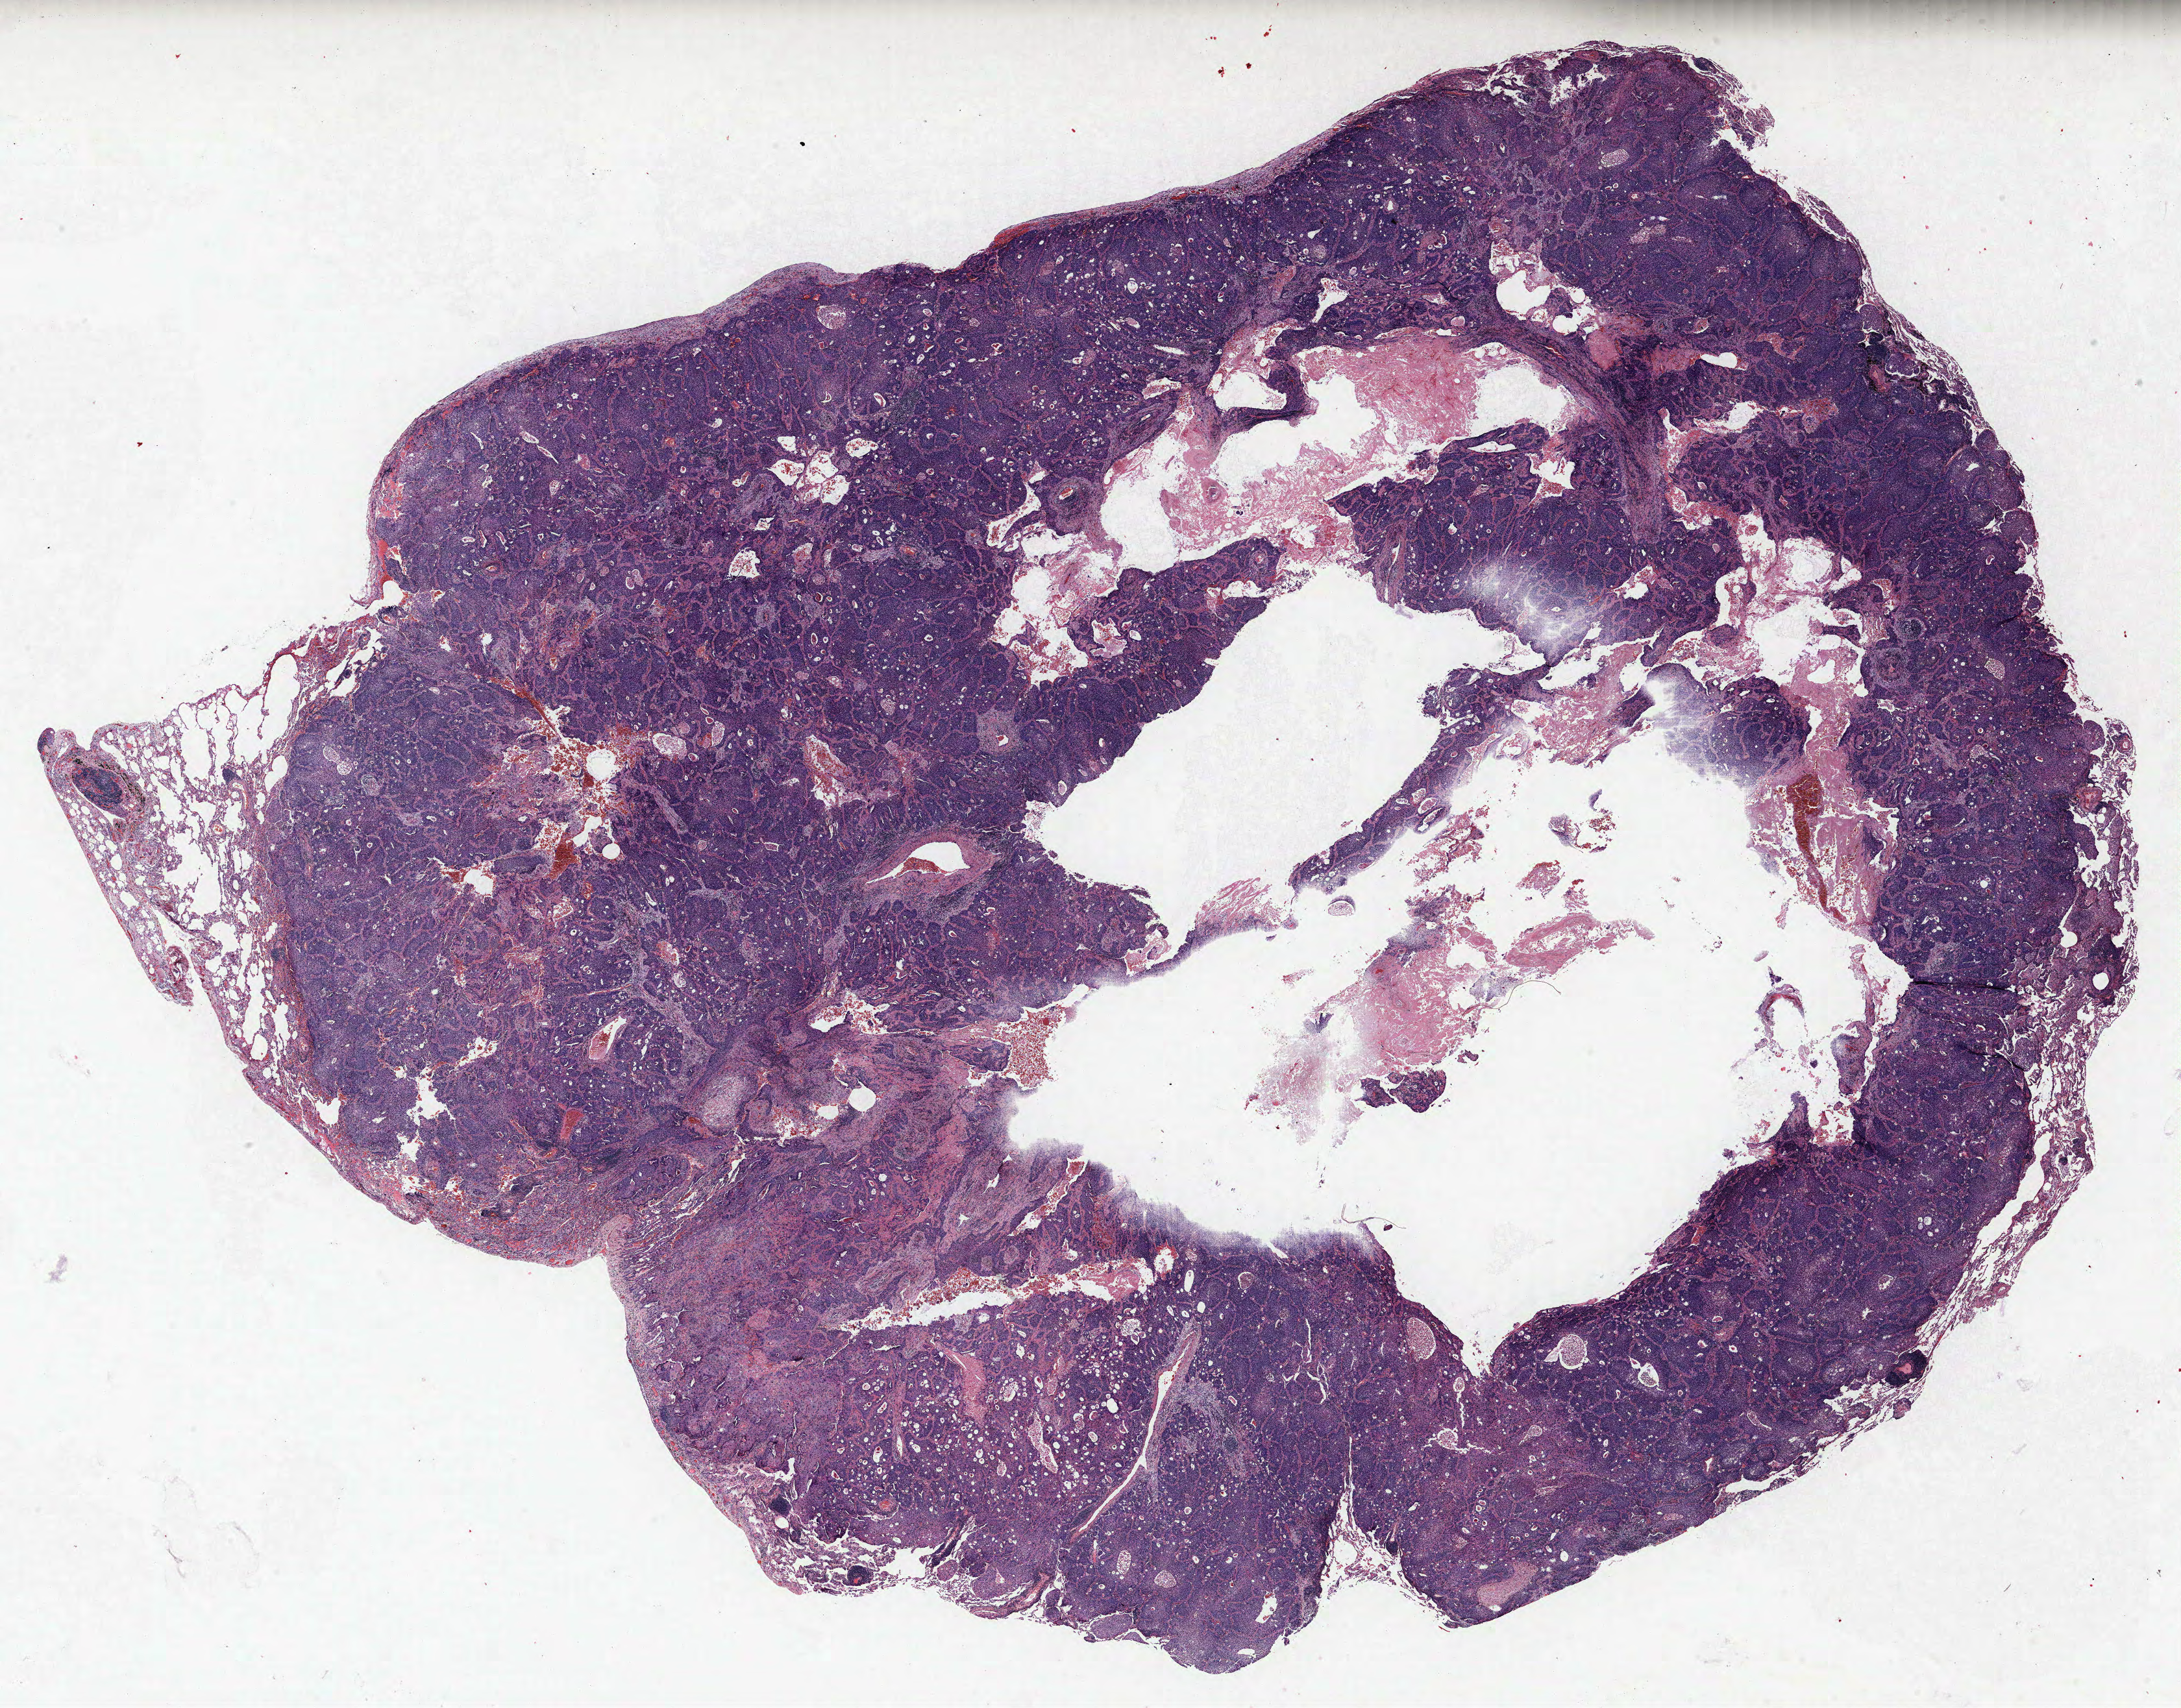
Hematoxylin and eosin (H&E) stained whole-slide image — low-resolution overview of the scanned area, about 26.9 x 21.1 mm (from a 40x scan); FFPE section; lung. Male, age 67 at enrolment. Grade: moderately differentiated (G2).
• tumour size (pathology): 25 mm
• stage (AJCC 6th edition): IB
• primary tumour location (clinical record): left upper lobe
• participant's lung-cancer diagnosis: Squamous cell carcinoma, NOS (ICD-O-3 8070/3)